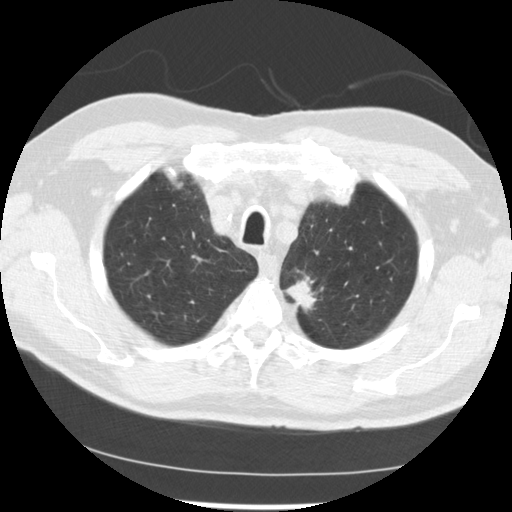
Axial slice from a low-dose chest CT screening exam, first (baseline) screen, lung window (W 1500 / L -600 HU), 512 × 512 image matrix. Male participant, aged 71 years at enrolment.
Expert-annotated lung lesion, box from (x=272, y=268) to (x=336, y=318) px. The screening reader recorded 2 non-calcified nodules or masses ≥4 mm on this exam (left upper lobe, left upper lobe); which of them this box marks is not recorded. Later outcome: lung cancer diagnosed 37 days after this screen — adenocarcinoma, NOS, left upper lobe, poorly differentiated (G3), stage IIIB (AJCC 6th edition), 25 mm at pathology.